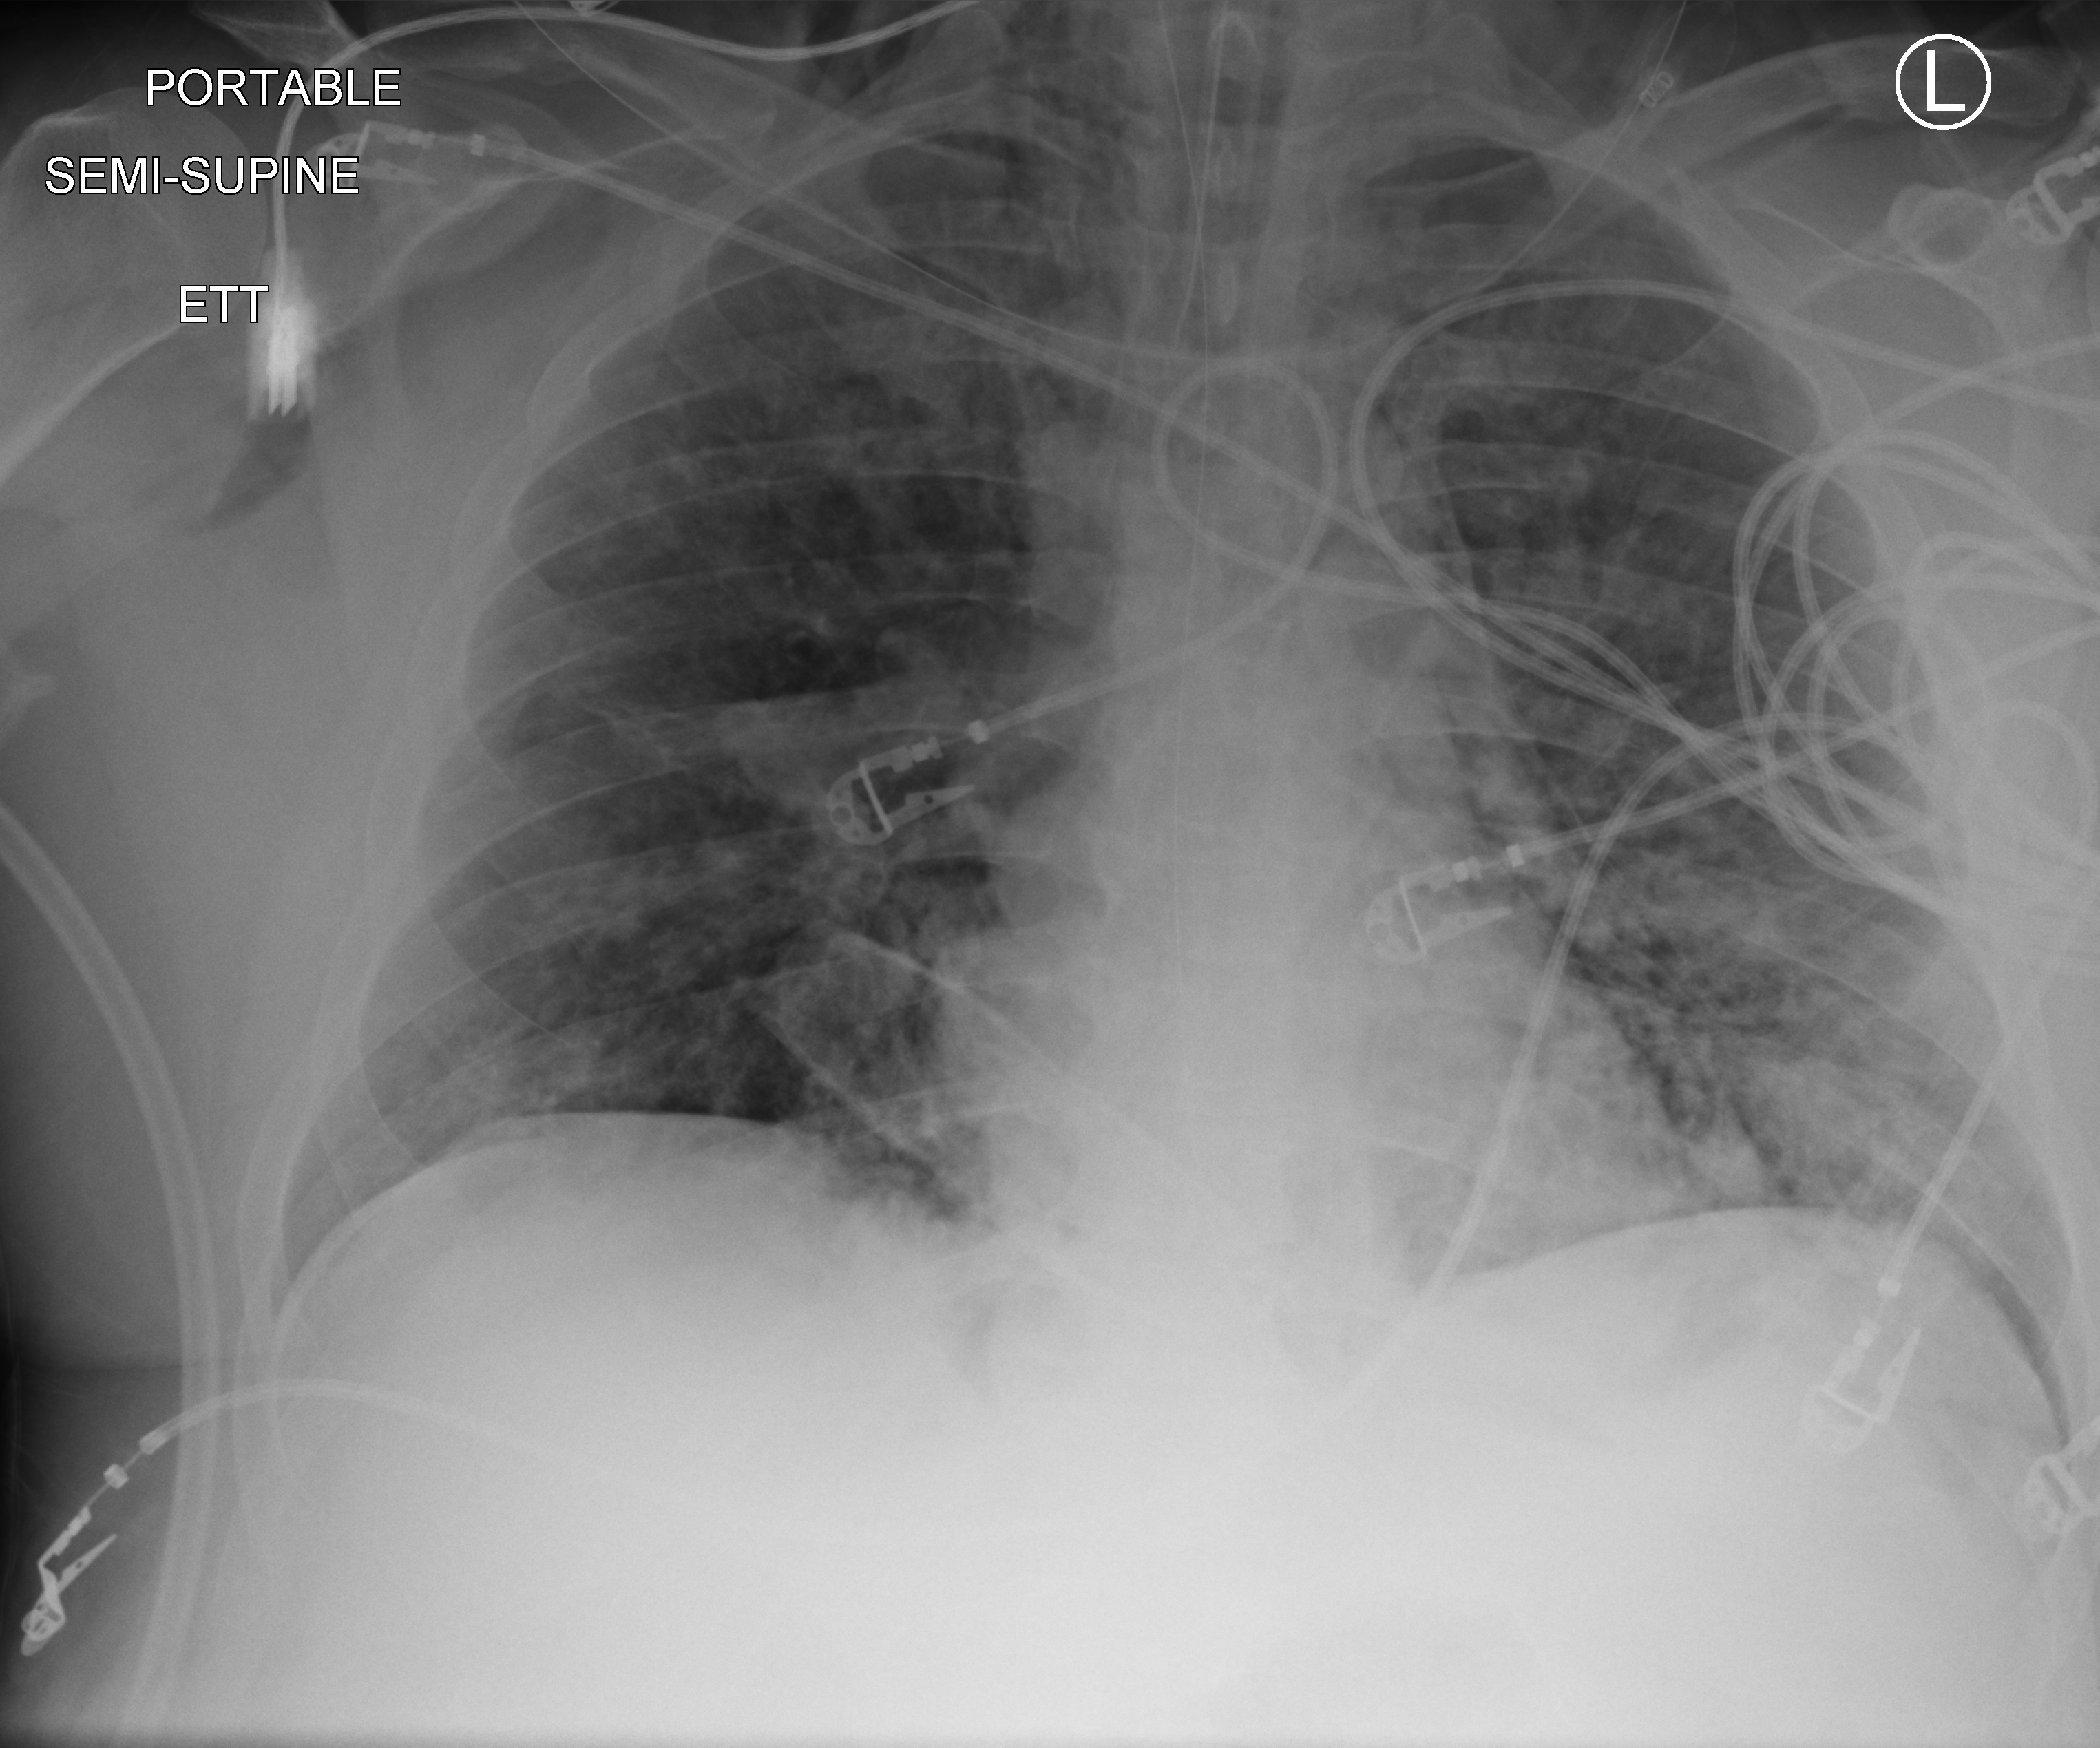
Bedside chest radiograph (computed radiography); anteroposterior (AP) projection. Adult patient hospitalised with COVID-19, age 18–59 years.
From the hospital-stay record, not from the radiograph (when in the stay this image was taken is not recorded):
- mechanically ventilated during this hospital stay: yes